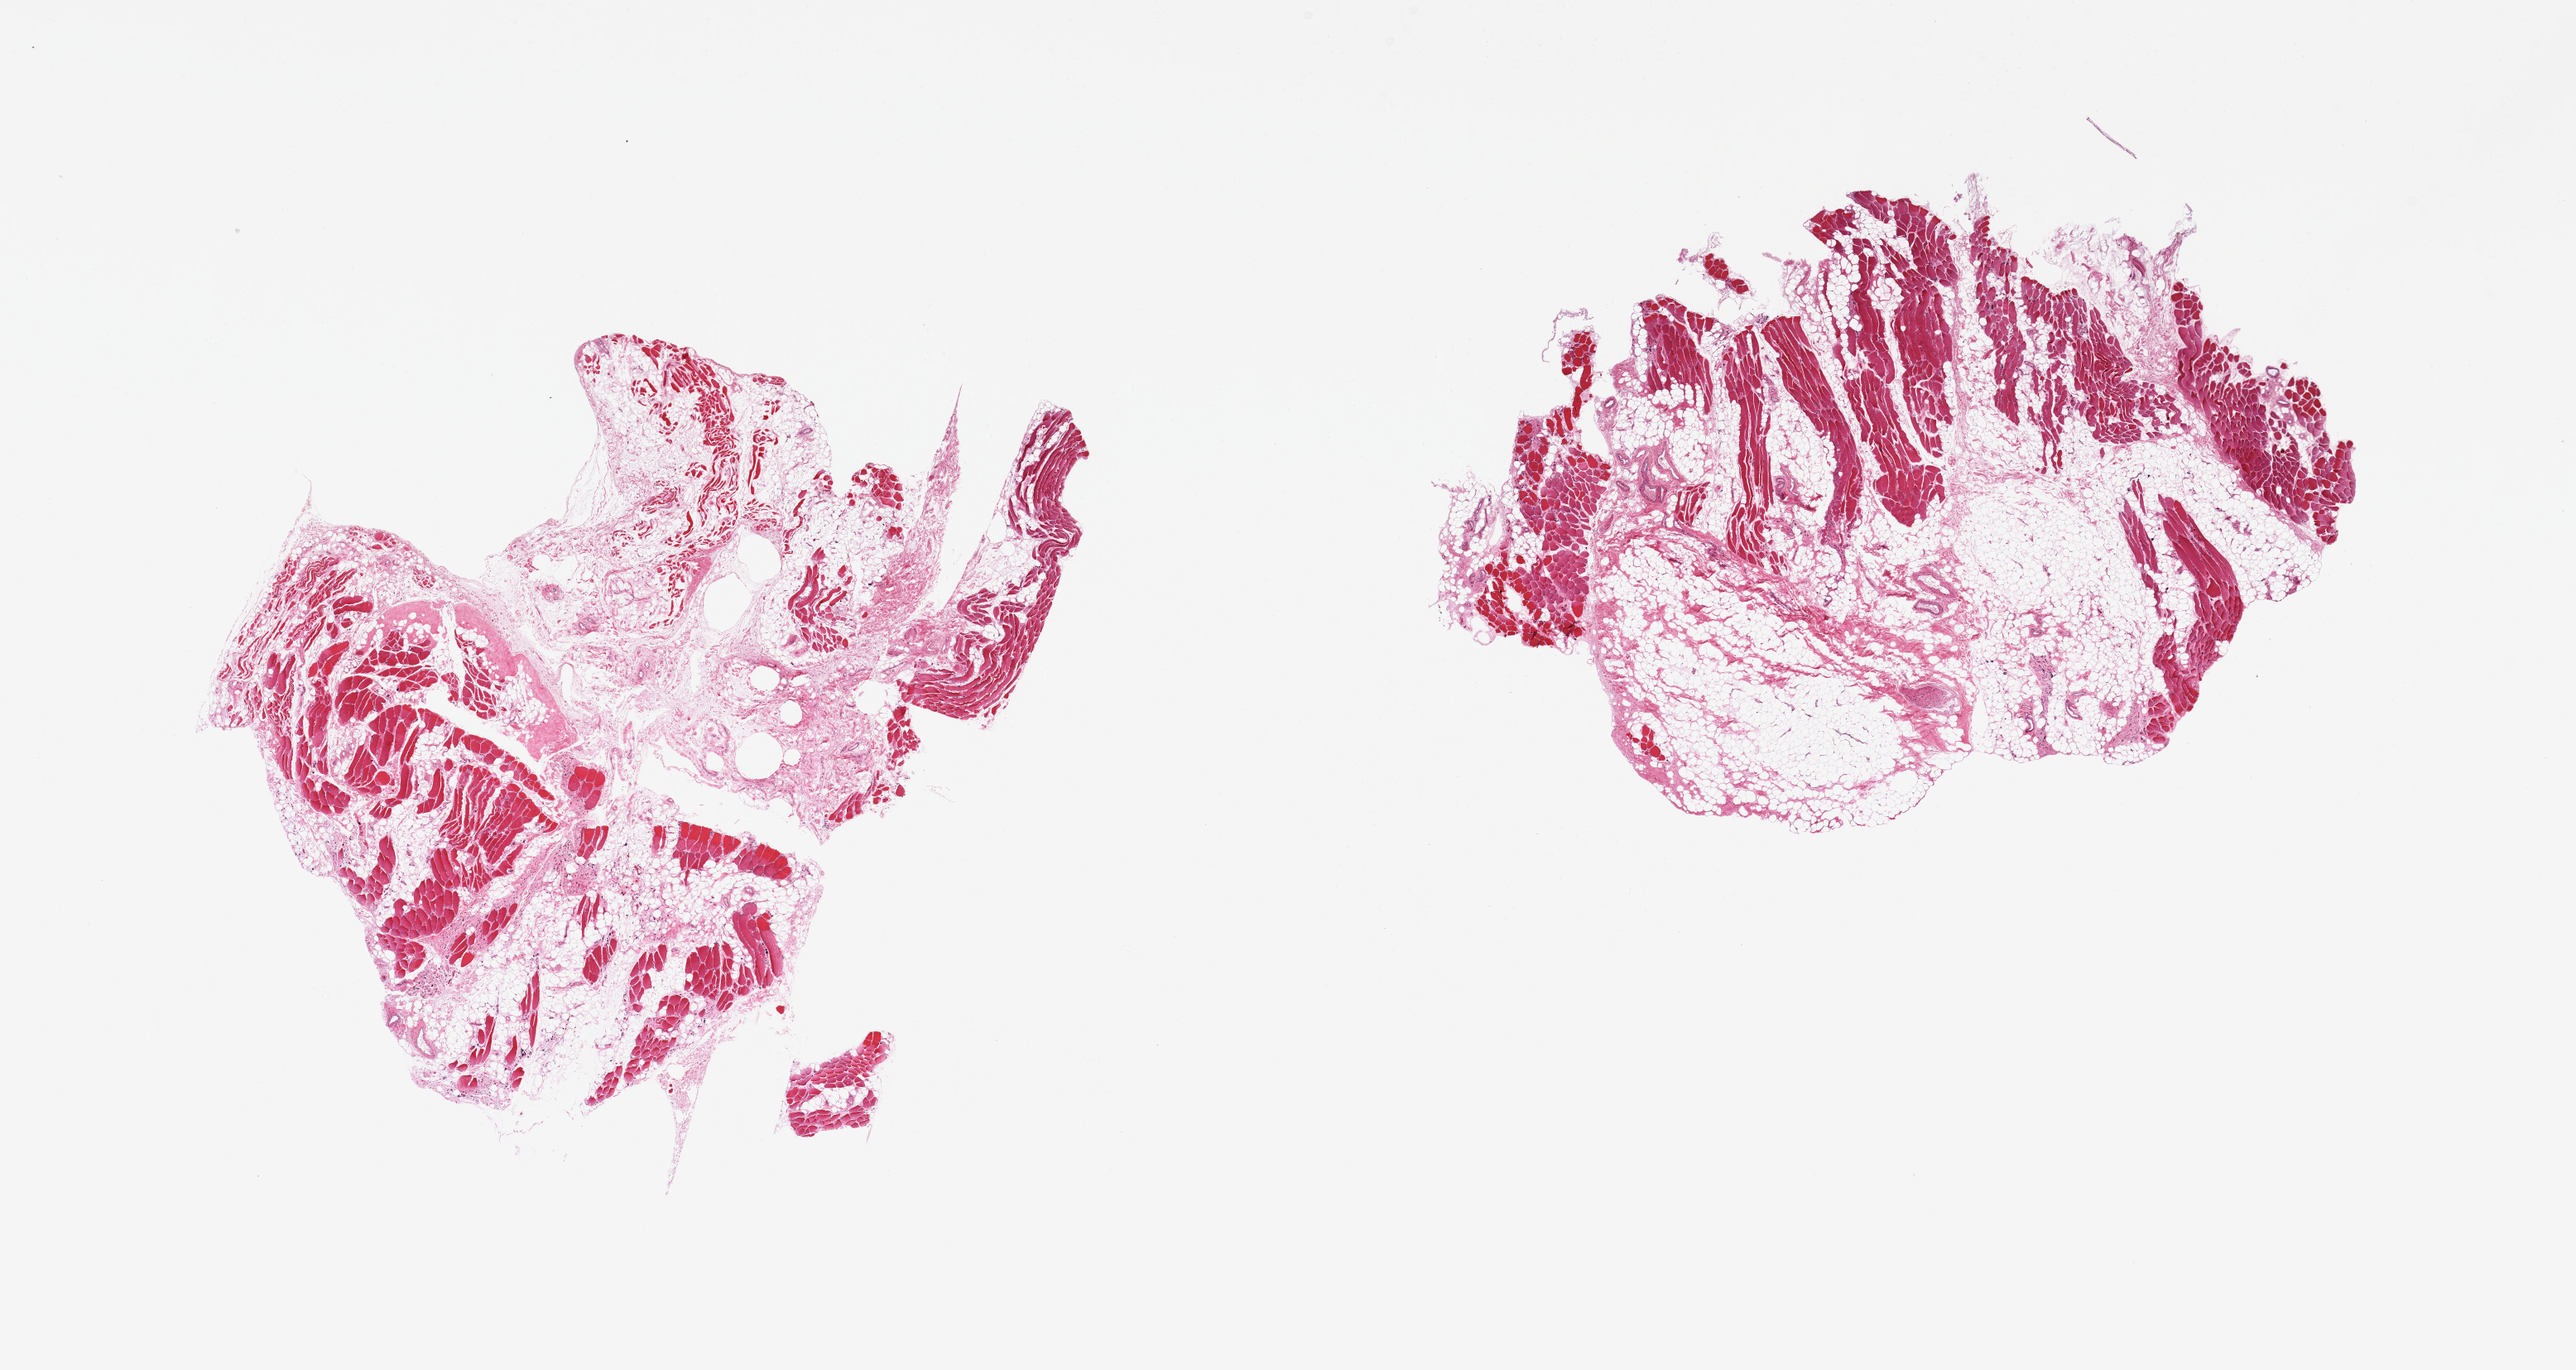
Whole-slide image, hematoxylin and eosin (H&E) stain — low-resolution overview of the scanned area, about 24.6 x 13.1 mm. PAXgene-fixed paraffin-embedded (PFPE) section. Sampled site (target tissue): skeletal muscle. Tissue donor sample. Donor: female.
- pathologist's review note for this sample: 2 pieces, ~70% adherent/interstitial fat; atrophic muscle